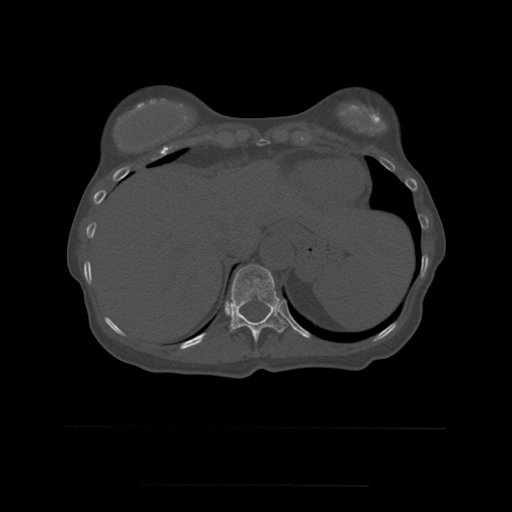
CT including the spine, one axial slice. Slice 282 of 544 in the series (ordered by position). Bone window (W 1800 / L 400 HU). 1.25 mm slice thickness. 512 × 512 image matrix, field of view 350 × 350 mm. Patient age 58 years. Case-level facts recorded for this patient, not image findings: primary cancer: lung.
Structures marked on this image (semi-automatic segmentation, software-assisted and operator-edited):
- T11 vertebra: bounding box [x1, y1, x2, y2] px = [227, 265, 288, 342]